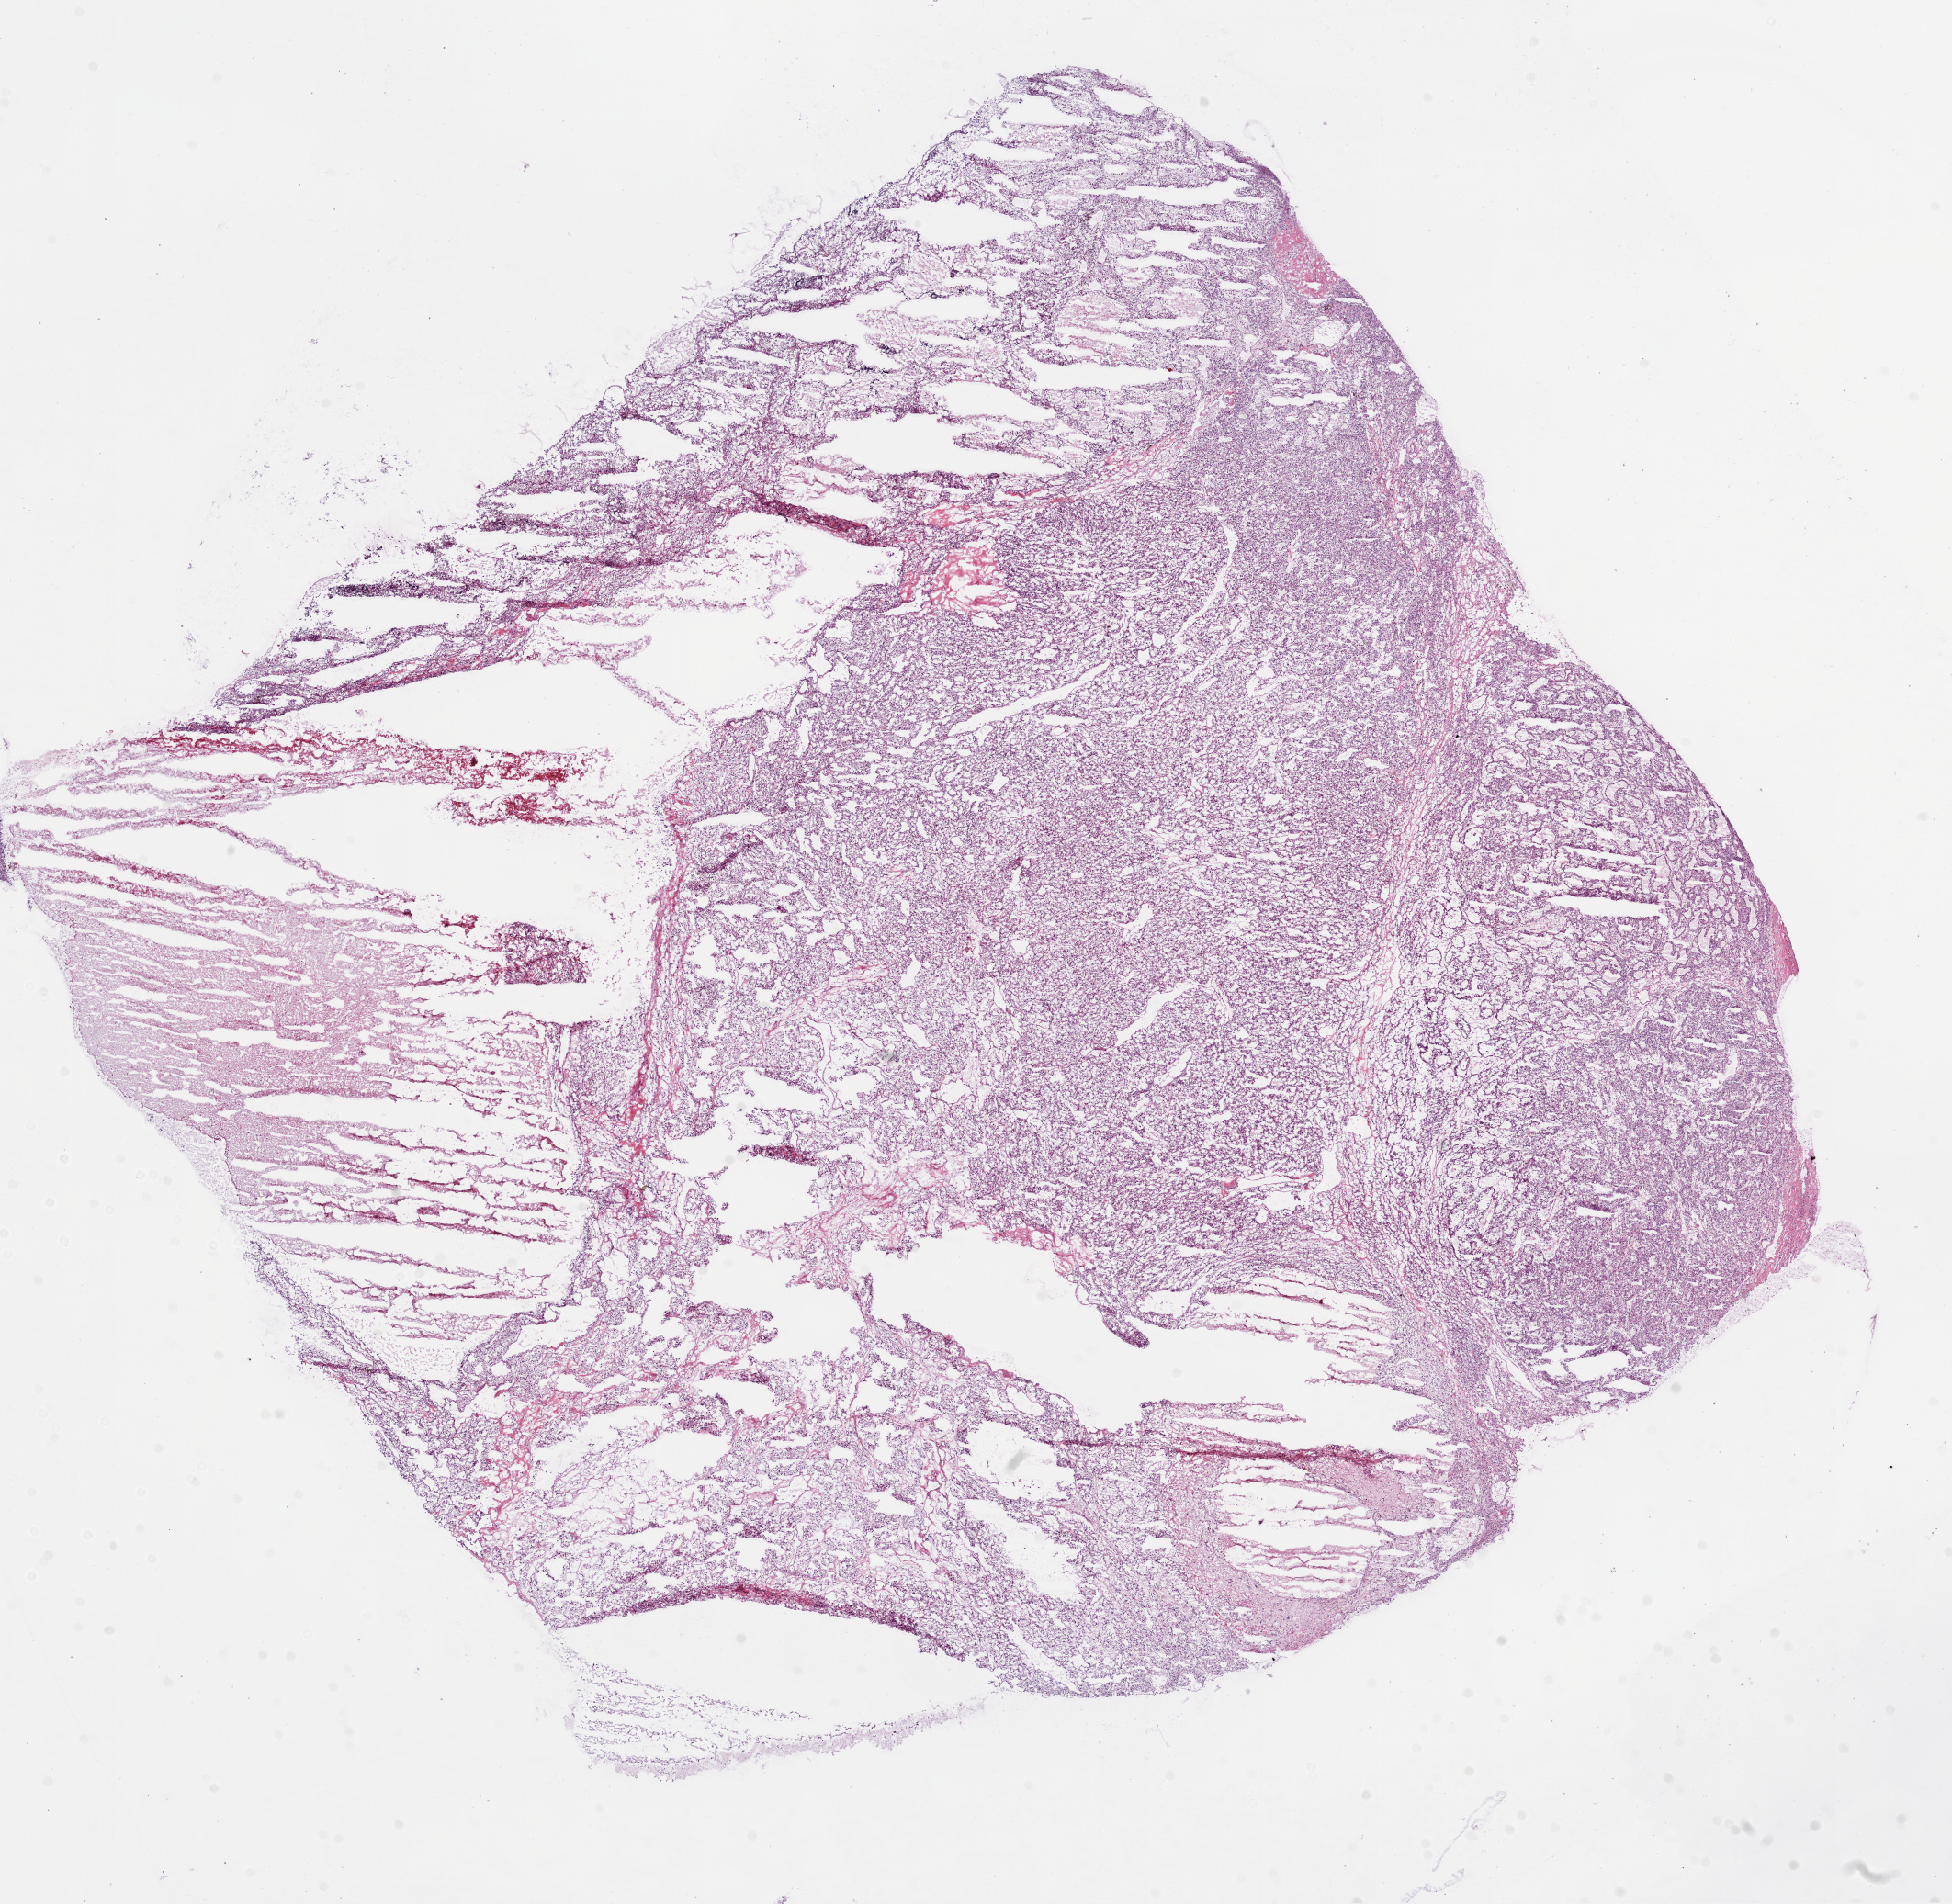
Whole-slide histology image, H&E-stained — a low-resolution overview of the entire scanned area, about 17.1 x 16.6 mm (slide scanned at 20x). Frozen section from the bottom of the tissue portion. Primary tumour sample from the kidney. Male, age 40 years at initial diagnosis. Histologic grade: G3 (poorly differentiated). Slide review estimates, as recorded: tumour cells 80%, tumour nuclei 85%, normal cells 0%, stromal cells 15%, necrosis 5%.
- diagnosis: Clear cell adenocarcinoma, NOS
- lymph nodes positive (case pathology): 0 of 3 examined
- laterality: right
- AJCC pathologic stage: I
- TNM: T1b N0 M0